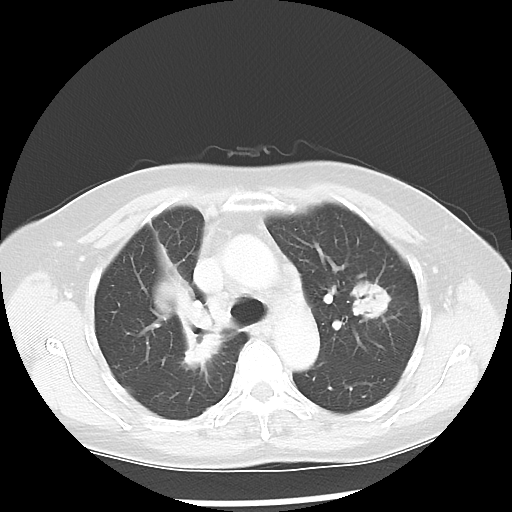
Chest CT, one axial slice. Position 35 of 52 along the scan axis. Reconstruction kernel LUNG. 100 kVp. Lung window (W 1500 / L -600 HU). 5 mm slice thickness. 512 × 512 image matrix, field of view 328 × 328 mm. Patient: female, 60 years. From the clinical record (not read from this slice): clinical TNM (as recorded): T2 N1 M1a.
Structures marked on this image (rectangle marked by the reading radiologist):
- lung tumour (recorded histology: adenocarcinoma): bounding box [x1, y1, x2, y2] px = [151, 271, 227, 381]